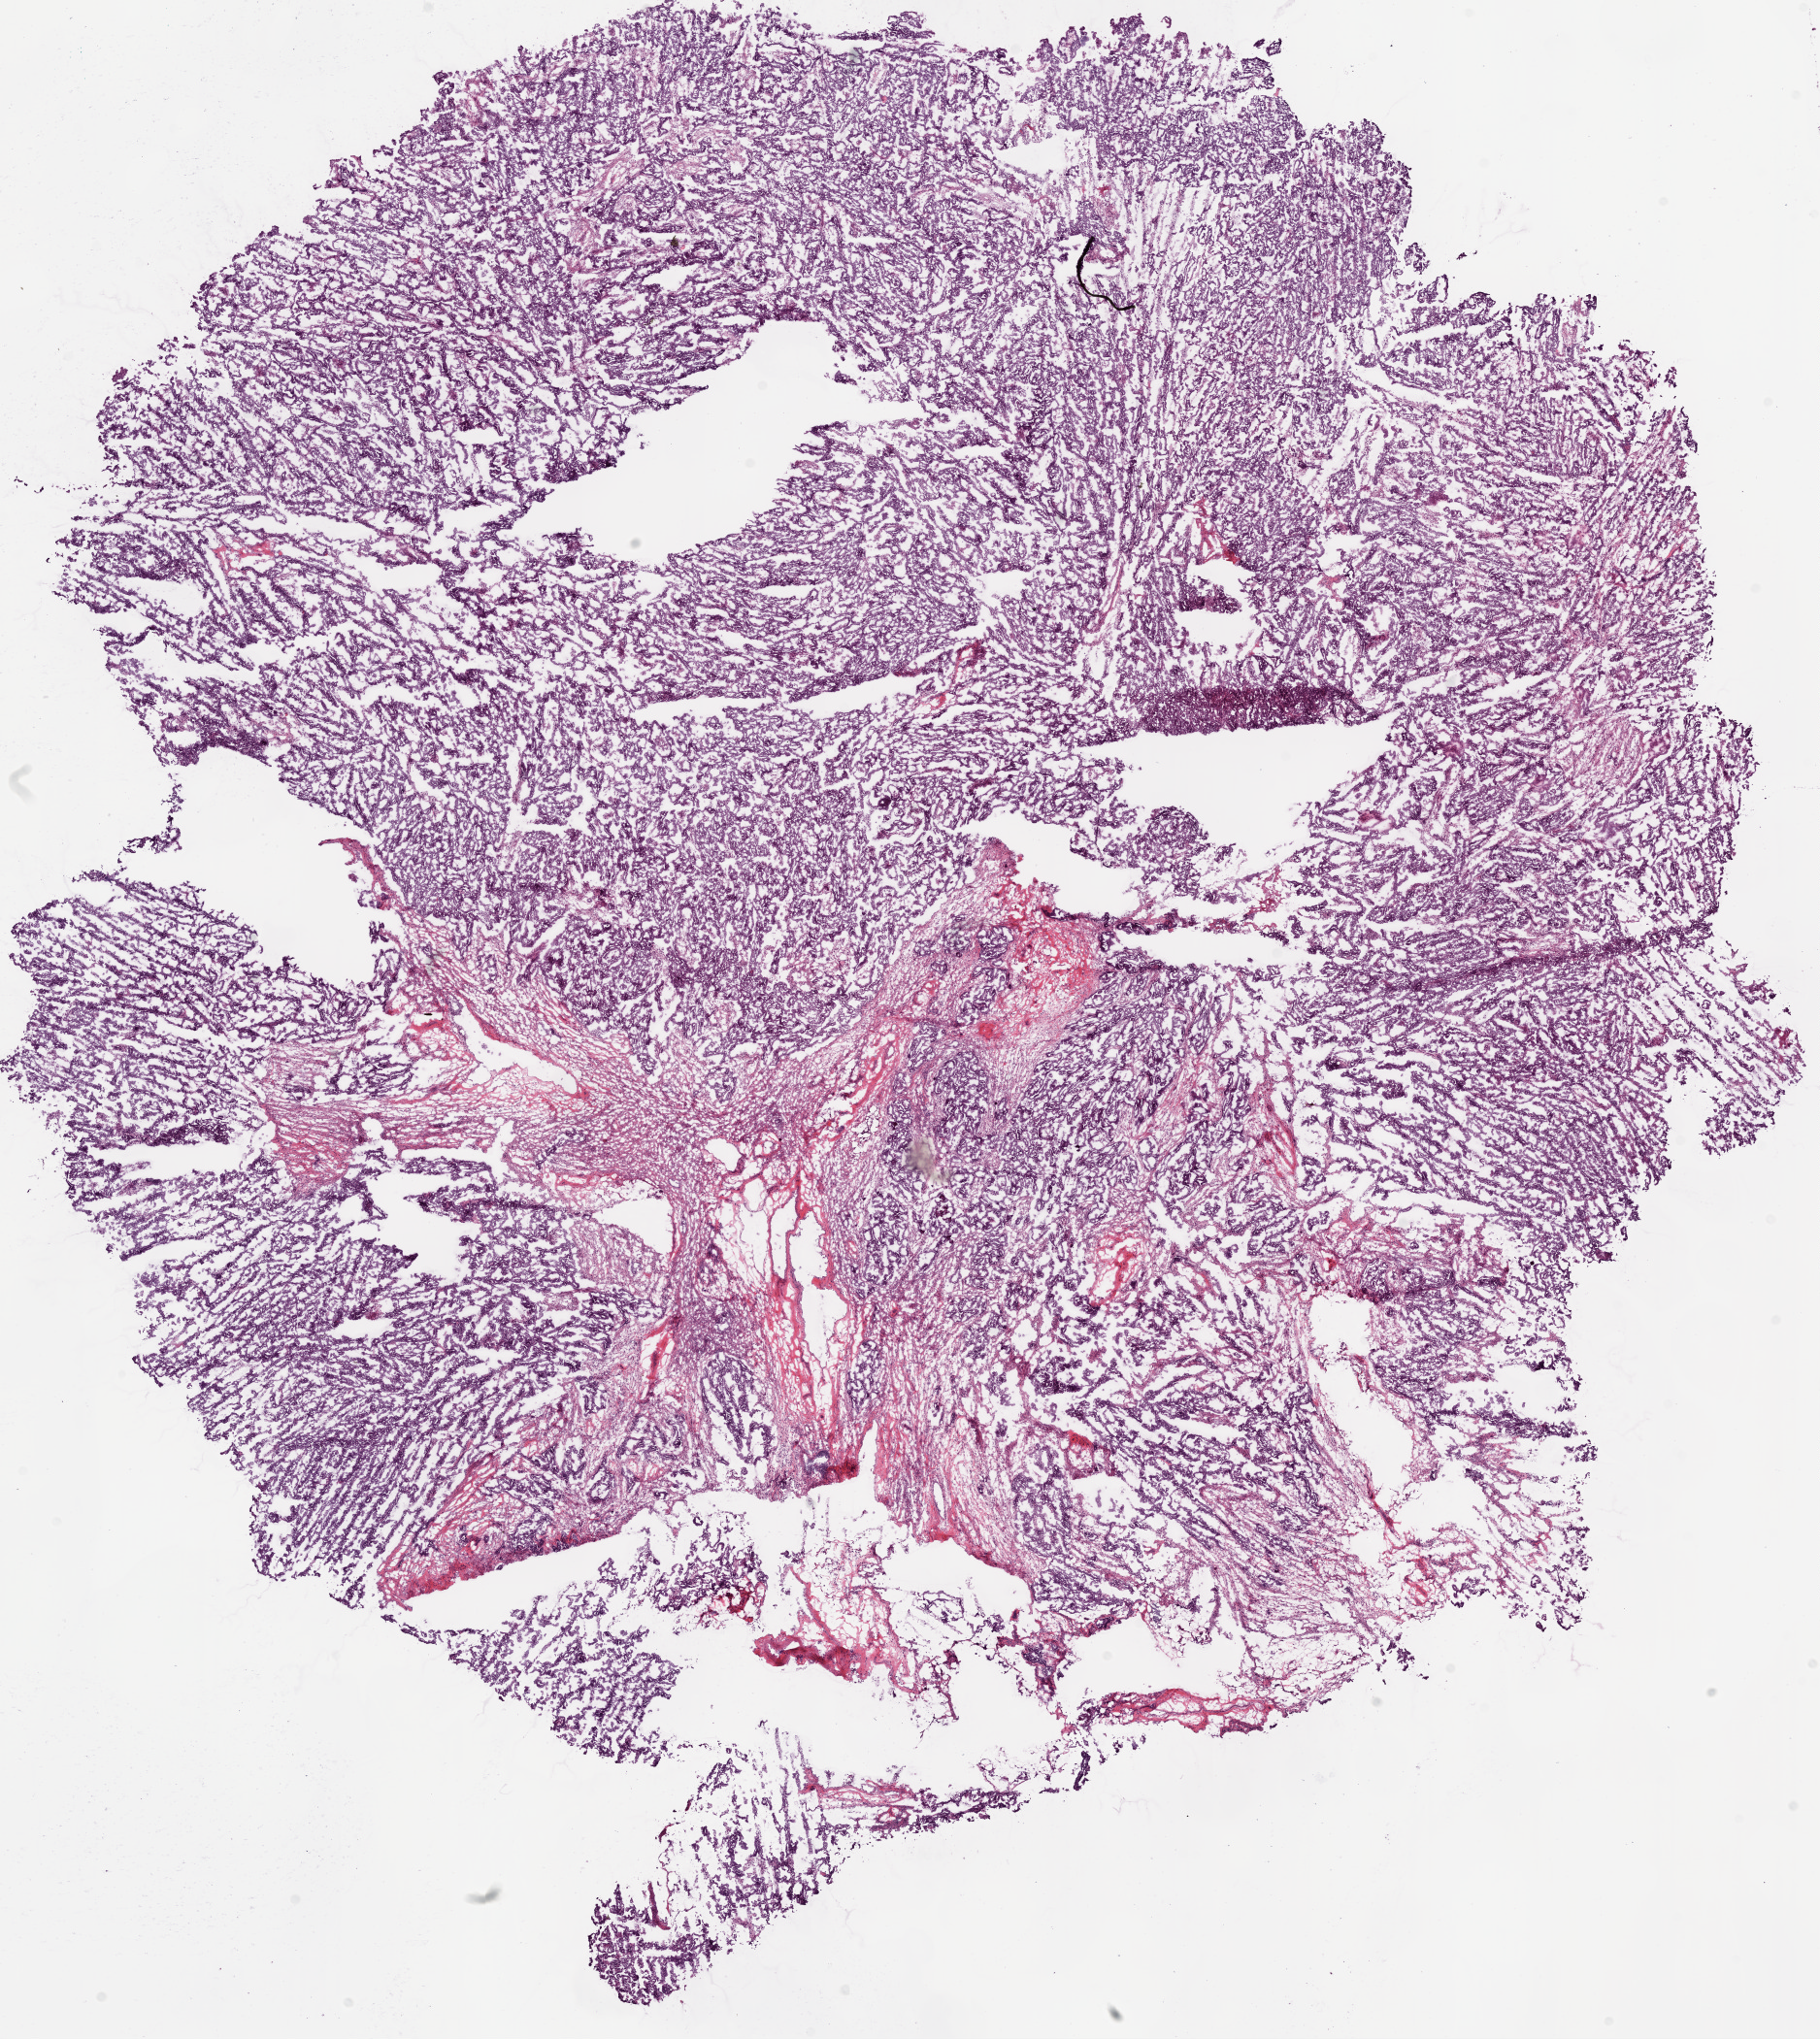
Whole-slide histology image, Hematoxylin and eosin (H&E) stained — shown as a low-resolution overview of the whole scanned area (about 15.0 x 16.9 mm), frozen section, sample: primary tumour, ovary. Female, age 52 years at initial diagnosis. Histologic grade: G2 (moderately differentiated). Pathologist review of this section (percent, as recorded): tumour cells 80%, tumour nuclei 85%, normal cells 0%, stromal cells 20%, necrosis 0%. Infiltration values recorded for this section: lymphocyte infiltration 65%, monocyte infiltration 5%, neutrophil infiltration 30%.
FIGO stage: IV. Diagnosis: Serous cystadenocarcinoma, NOS.